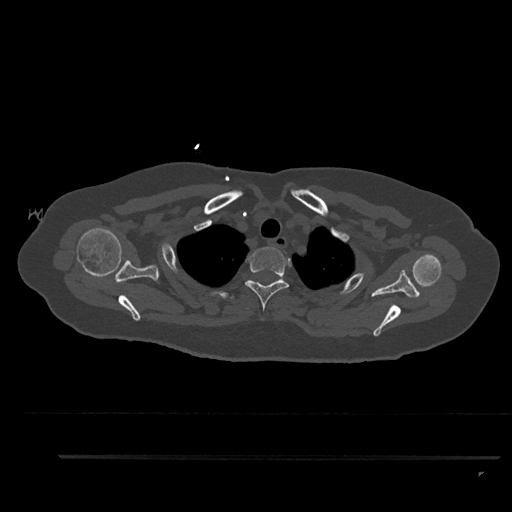
CT including the spine, one axial slice; position 720 of 797 along the scan axis; bone window (W 1800 / L 400 HU); 0.5 mm slice thickness; 512 × 512 image matrix, field of view 408 × 408 mm. Female patient, age 44 years. Case-level facts recorded for this patient, not image findings: primary cancer: renal; vertebrae with lytic lesions (as recorded): L1.
Structures marked on this image (semi-automatic segmentation, software-assisted and operator-edited):
- T2 vertebra: bounding box (x1, y1, x2, y2) in pixels: (245, 247, 290, 311)